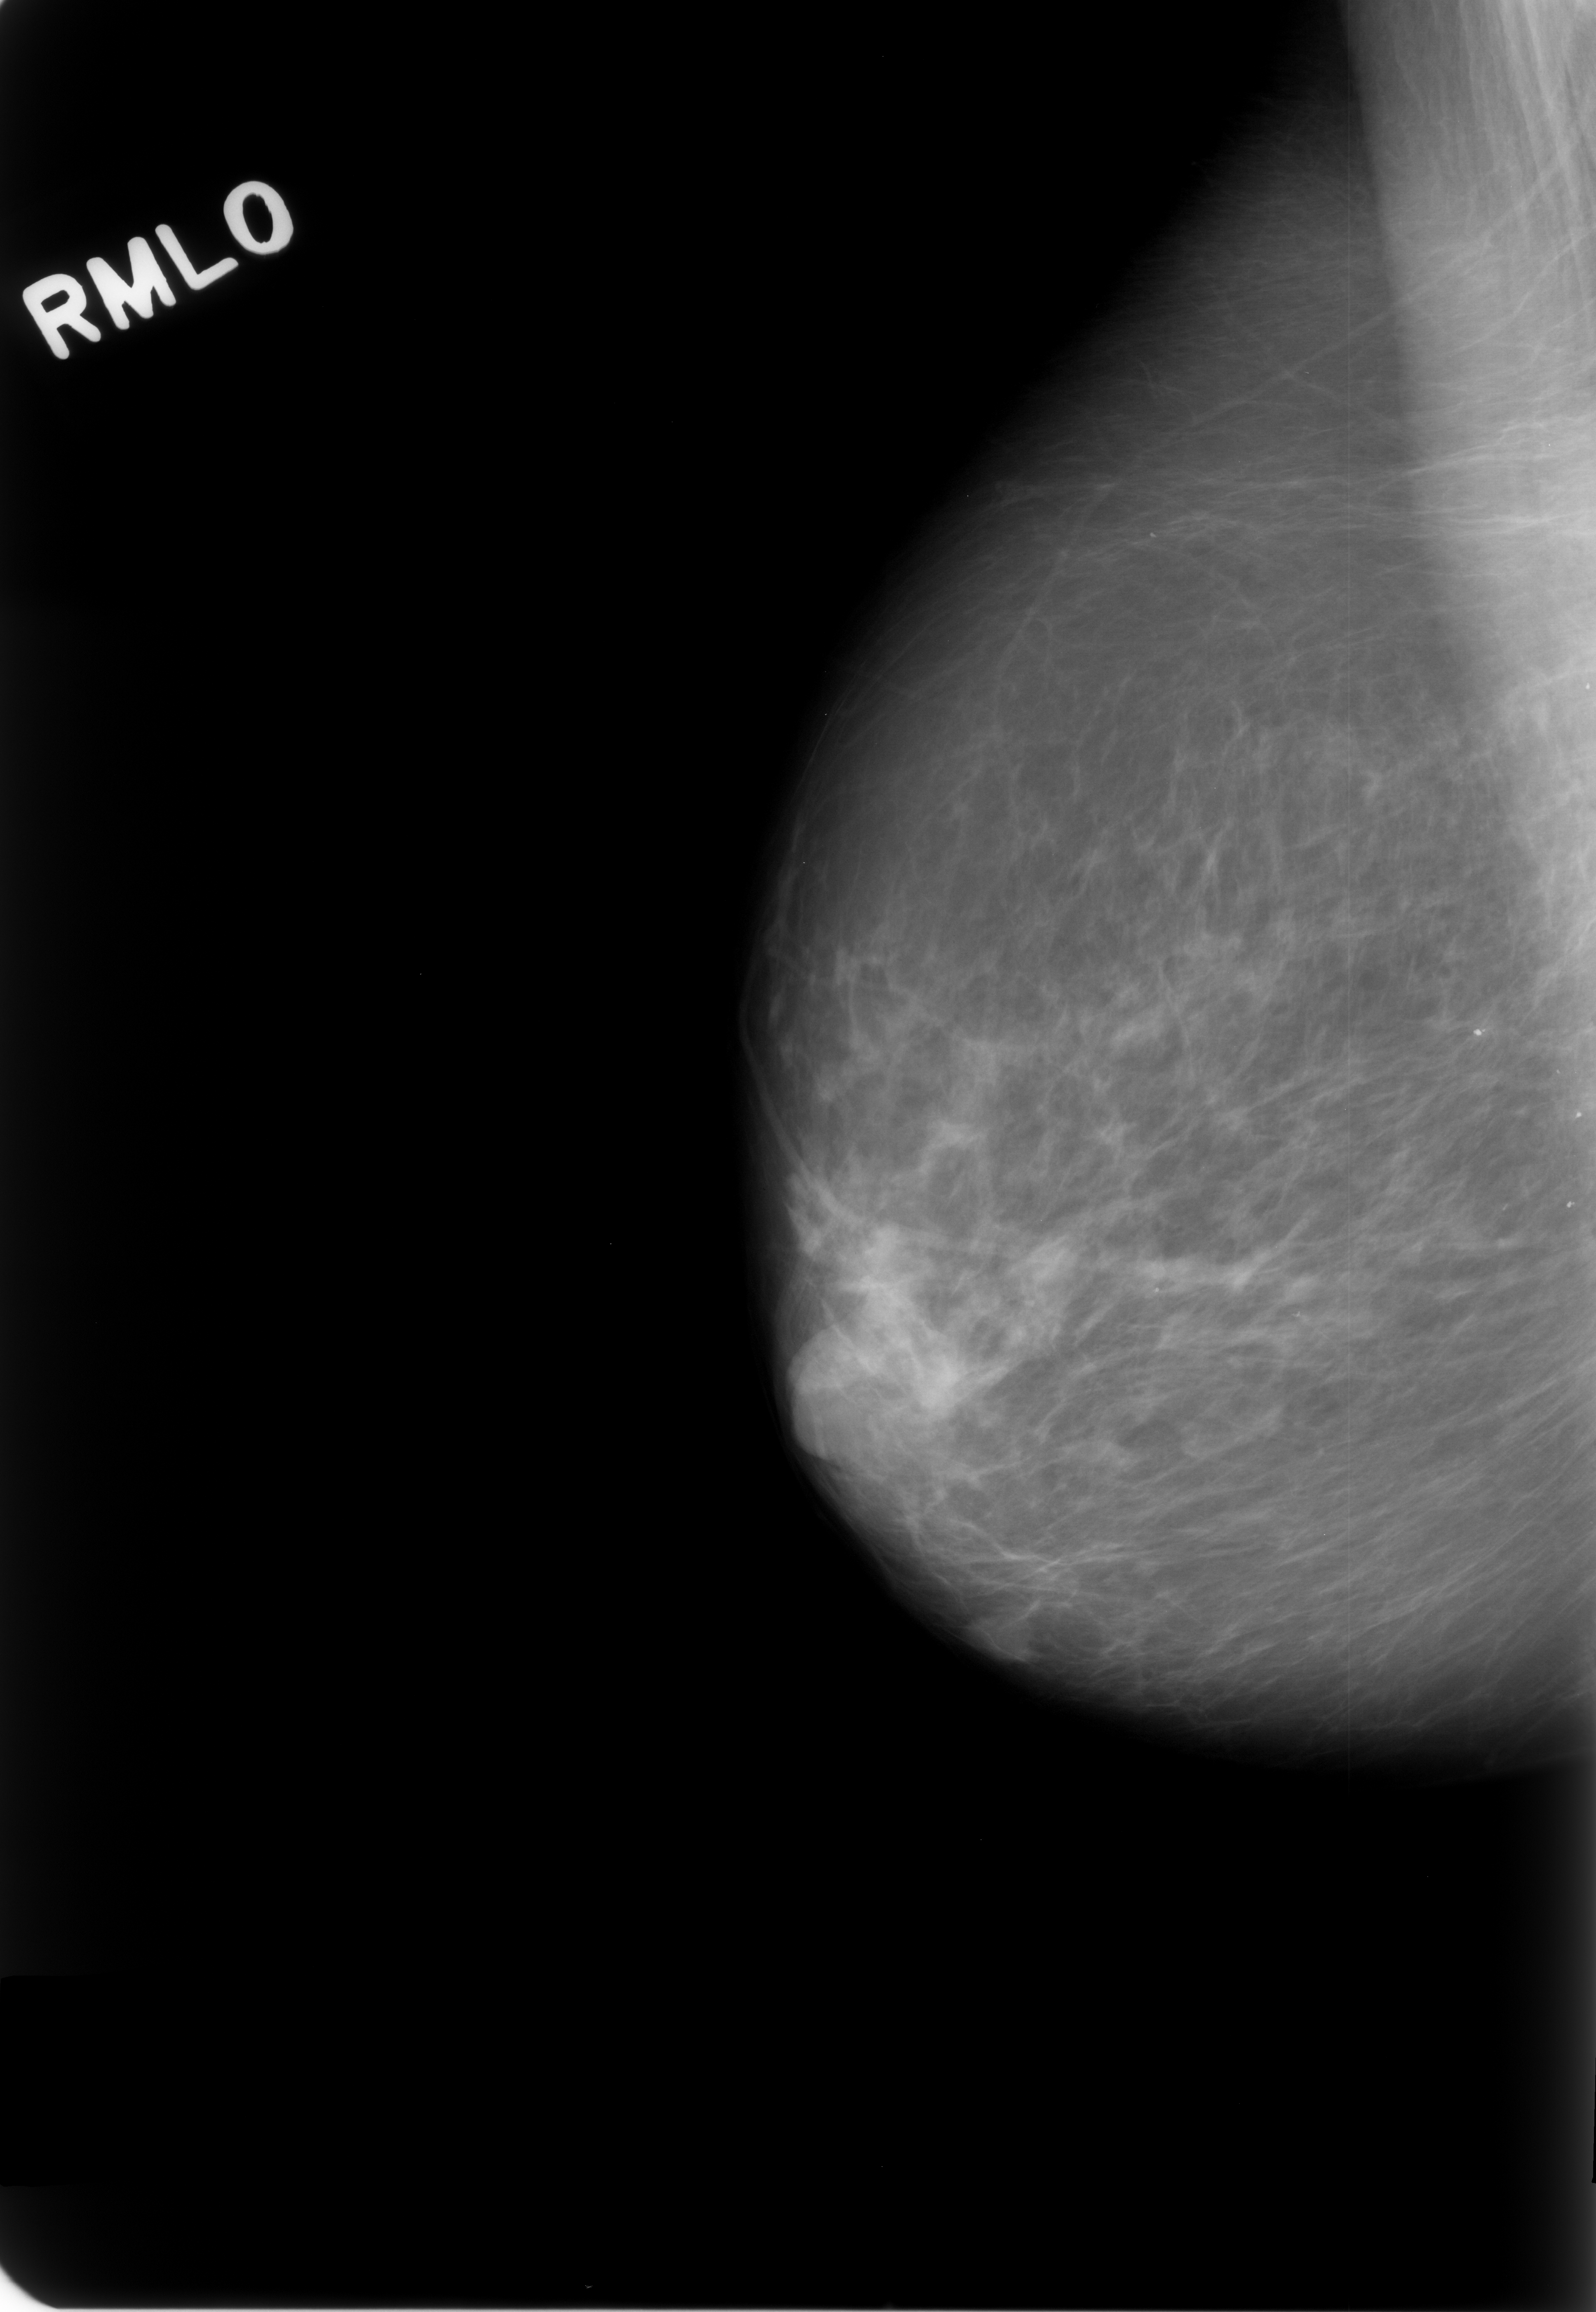
Digitized screen-film mammogram. Right breast. MLO view. BI-RADS breast density category 2 (scale 1–4). 1596 × 2312 image matrix.
Marked abnormalities (boxes around the expert regions of interest):
- mass, shape oval, margins circumscribed; BI-RADS assessment category 3; benign; no additional work-up was recommended (outcome (as recorded, no biopsy): benign without callback): bounding box [x1, y1, x2, y2] px = [962, 1570, 1070, 1672]